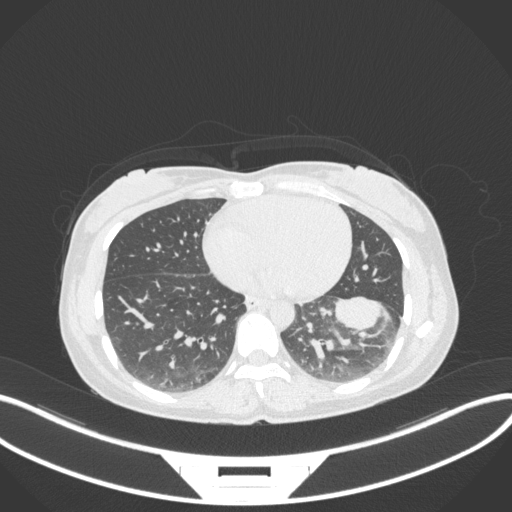
Chest CT, one axial slice. Reconstruction kernel B31f. 120 kVp. Lung window (W 1500 / L -600 HU). 1 mm slice thickness. 512 × 512 image matrix. Female patient, age 41 years. From the clinical record (not read from this slice): clinical TNM (as recorded): T2a N3 M1b.
Annotated regions visible in this slice (rectangle marked by the reading radiologist):
- lung tumour (recorded histology: adenocarcinoma): bounding box [x1, y1, x2, y2] px = [337, 294, 395, 339]